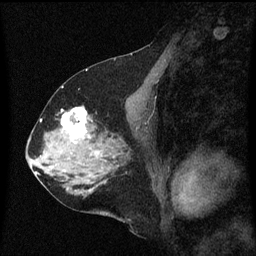
Breast MRI (dynamic contrast-enhanced), one sagittal slice. Slice 29 of 60 in the series (ordered by position). Dynamic contrast-enhanced series, image 2 of 3 at this slice position (ordered by acquisition). 1.5 T. TE 4.2 ms, TR 8 ms. 2 mm slice thickness. 256 × 256 image matrix. Patient: female, 58 years.
Annotated regions visible in this slice (semi-automatically segmented with operator editing):
- analysis volume of interest (the breast-tissue region the enhancement analysis was run in; not a lesion): bounding box (x1, y1, x2, y2) in pixels: (56, 106, 99, 149)
- tumour enhancement mask (voxels above the 70 % enhancement threshold inside the analysis volume of interest): (63, 108, 89, 139)